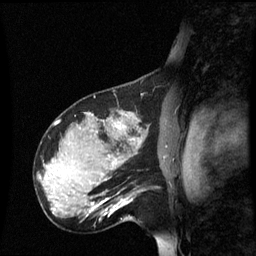
Breast MRI (dynamic contrast-enhanced), one sagittal slice; slice 43 of 60 in the series (ordered by position); dynamic contrast-enhanced series, image 2 of 3 at this slice position (ordered by acquisition); 1.5 T; TE 4.2 ms, TR 8.9 ms; 256 × 256 image matrix, field of view 220 × 220 mm. Patient: female, 31 years. From the clinical record (not read from this slice): setting: breast cancer imaged before/during neoadjuvant chemotherapy; receptor status: HR-positive, HER2-negative.
Outlined on this slice (semi-automatic segmentation, software-assisted and operator-edited):
- analysis volume of interest (the breast-tissue region the enhancement analysis was run in; not a lesion): bounding box <90,180,135,223> (left, top, right, bottom; pixels)
- tumour enhancement mask (voxels above the 70 % enhancement threshold inside the analysis volume of interest): <93,198,130,211>